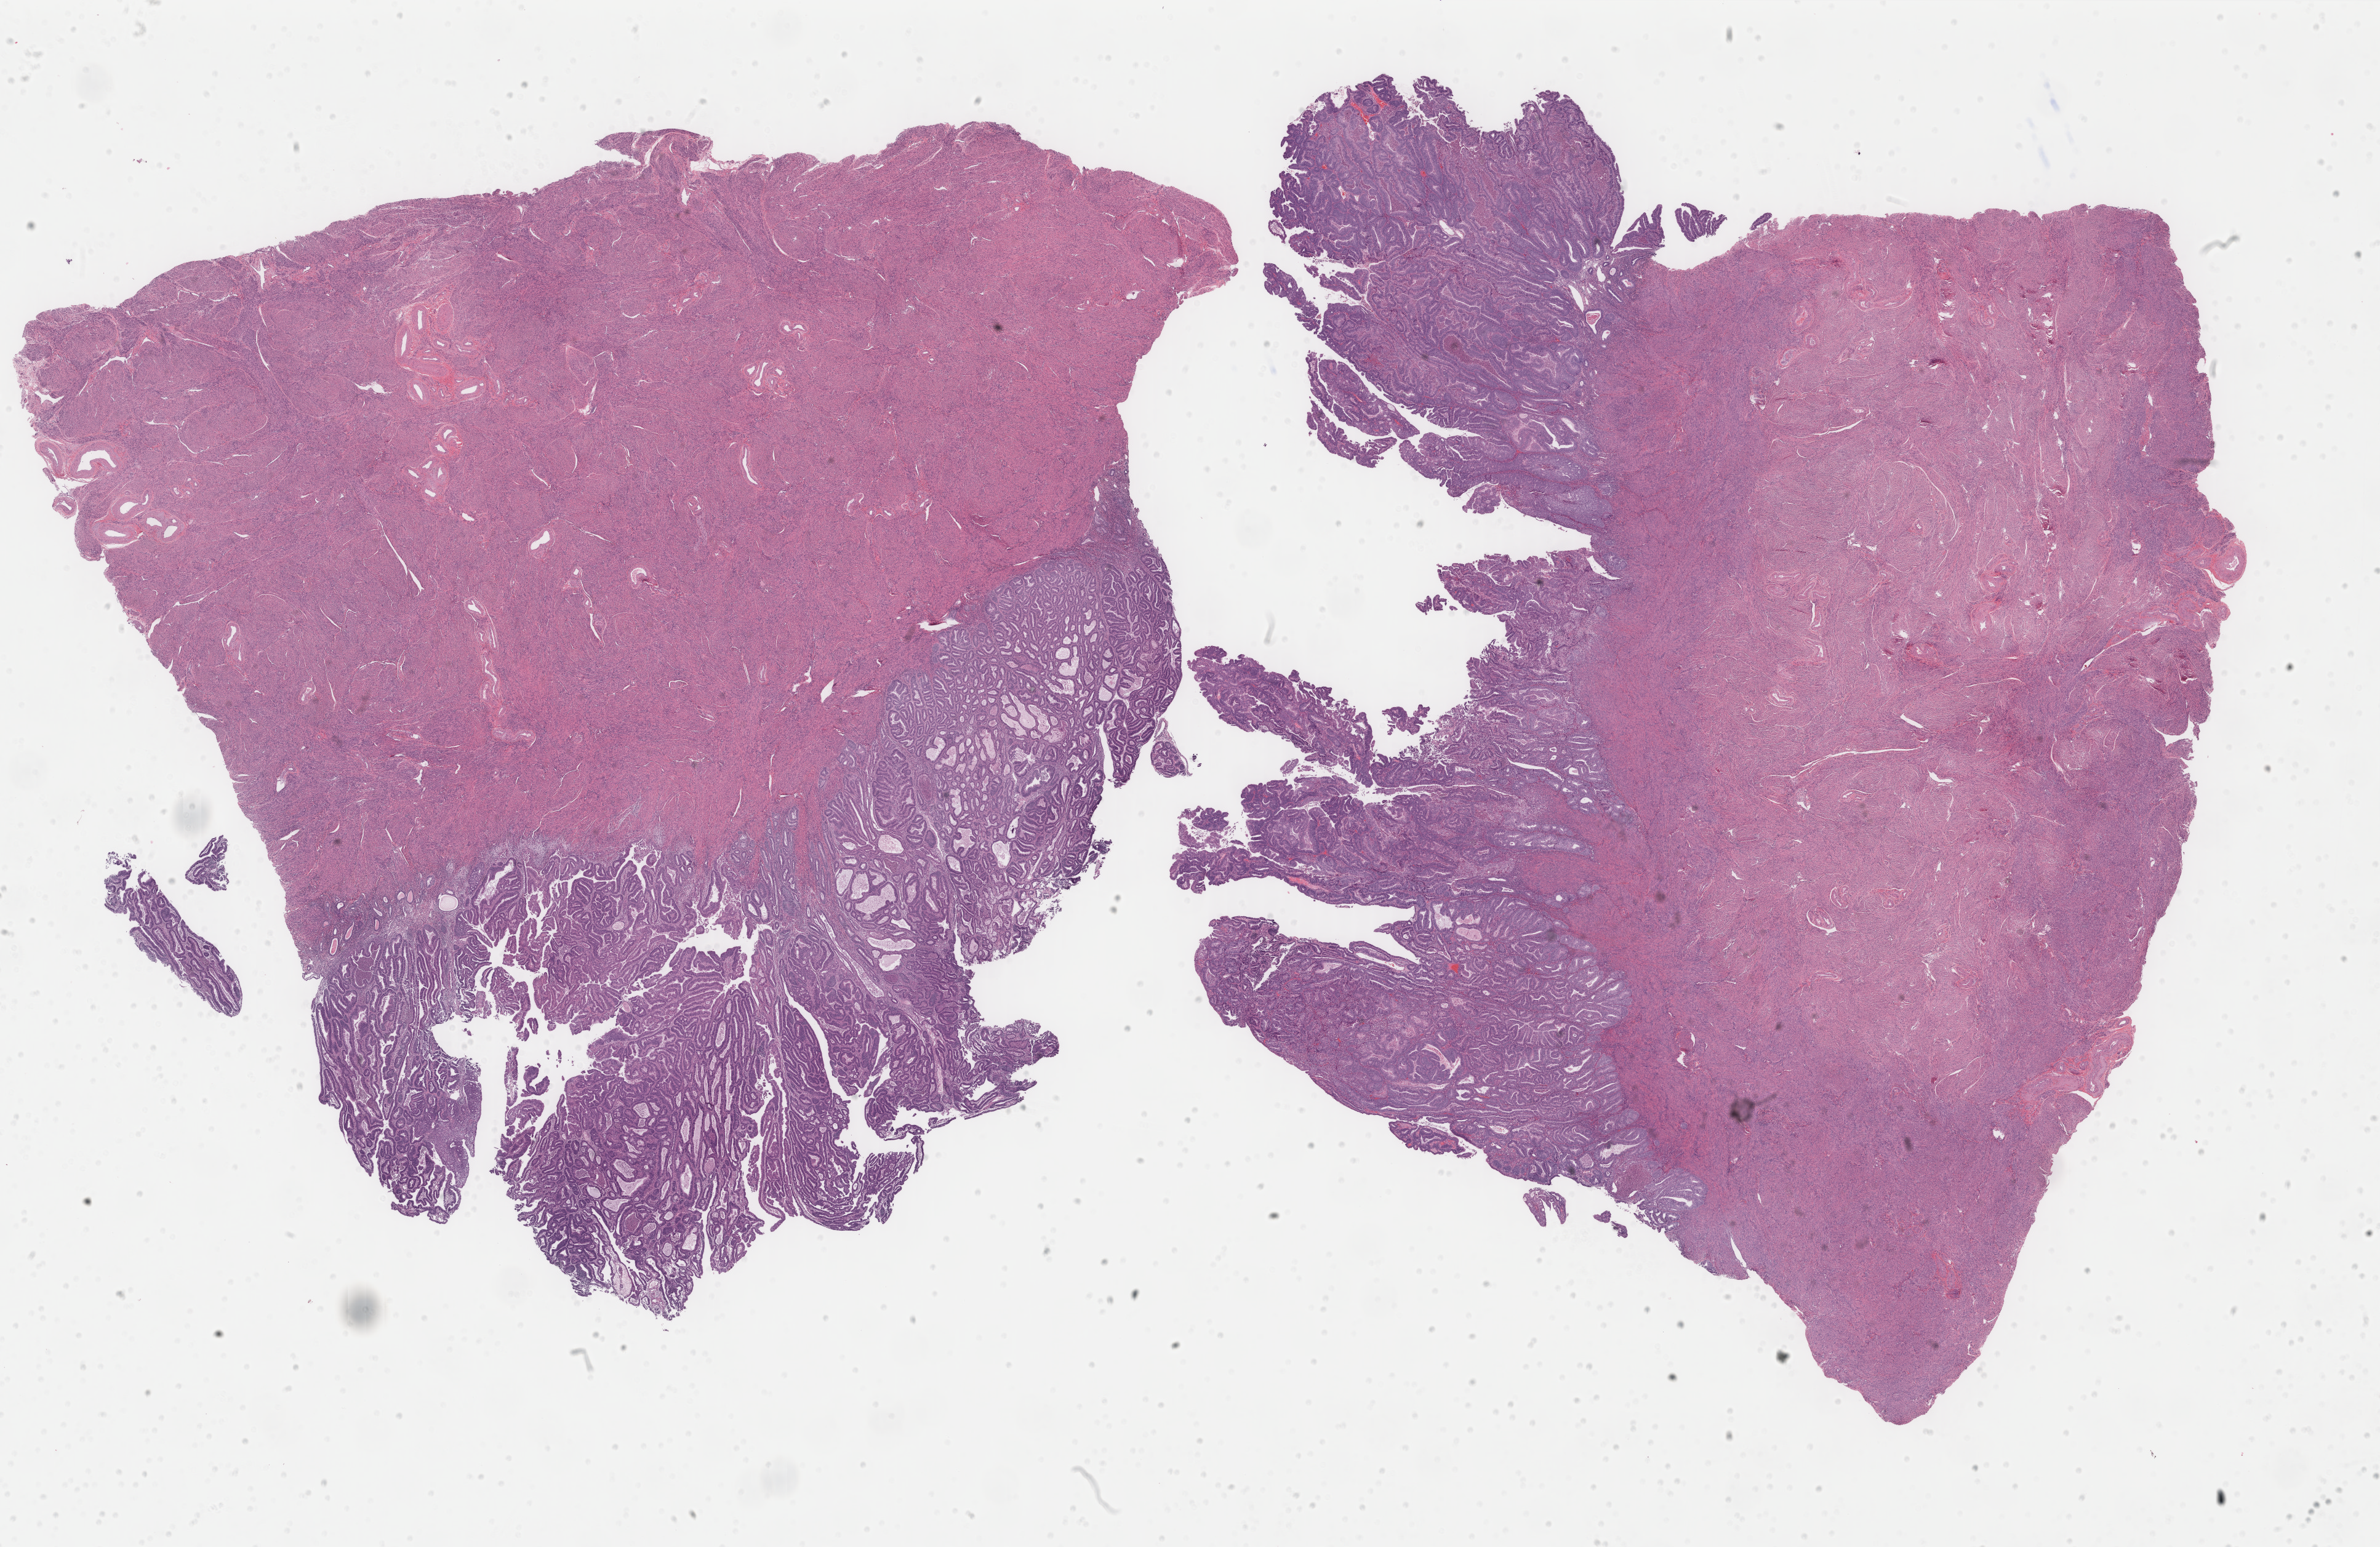
Whole-slide histology image, H&E — a low-resolution overview of the entire scanned area, about 30.7 x 20.0 mm; formalin-fixed paraffin-embedded (FFPE) diagnostic section; primary tumour sample from the uterus. Patient: female, age at initial diagnosis 60 years. Histologic grade: G1 (well differentiated).
Pathologic diagnosis: Endometrioid adenocarcinoma, NOS (endometrium). FIGO stage: IA.